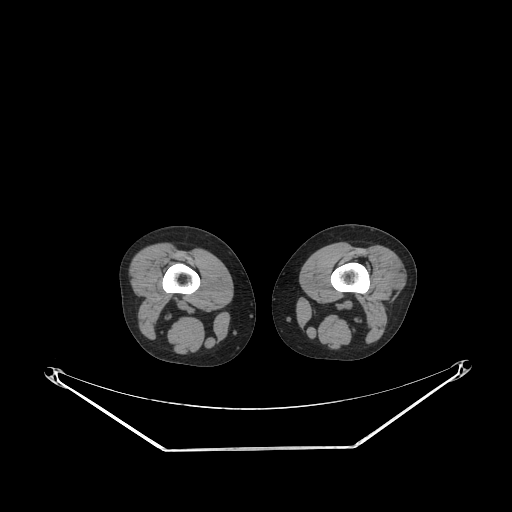
CT of an extremity soft-tissue mass (from a PET/CT study), one axial slice. Slice 180 of 223 in the series (ordered by position). Reconstruction kernel STANDARD. Soft-tissue window (W 400 / L 40 HU). 3.75 mm slice thickness. 512 × 512 image matrix, field of view 500 × 500 mm. Female patient. From the clinical record (not read from this slice): histological type: spindle cell suggestive of biphasic synovial sarcoma; grade: intermediate; site of the primary tumour: left knee.
Annotated regions visible in this slice (expert contour drawn on MRI and transferred to this co-registered scan by the dataset authors):
- gross tumour volume including surrounding oedema: bounding box <381,251,405,291> (left, top, right, bottom; pixels)
- gross tumour volume (mass): <381,251,405,291>